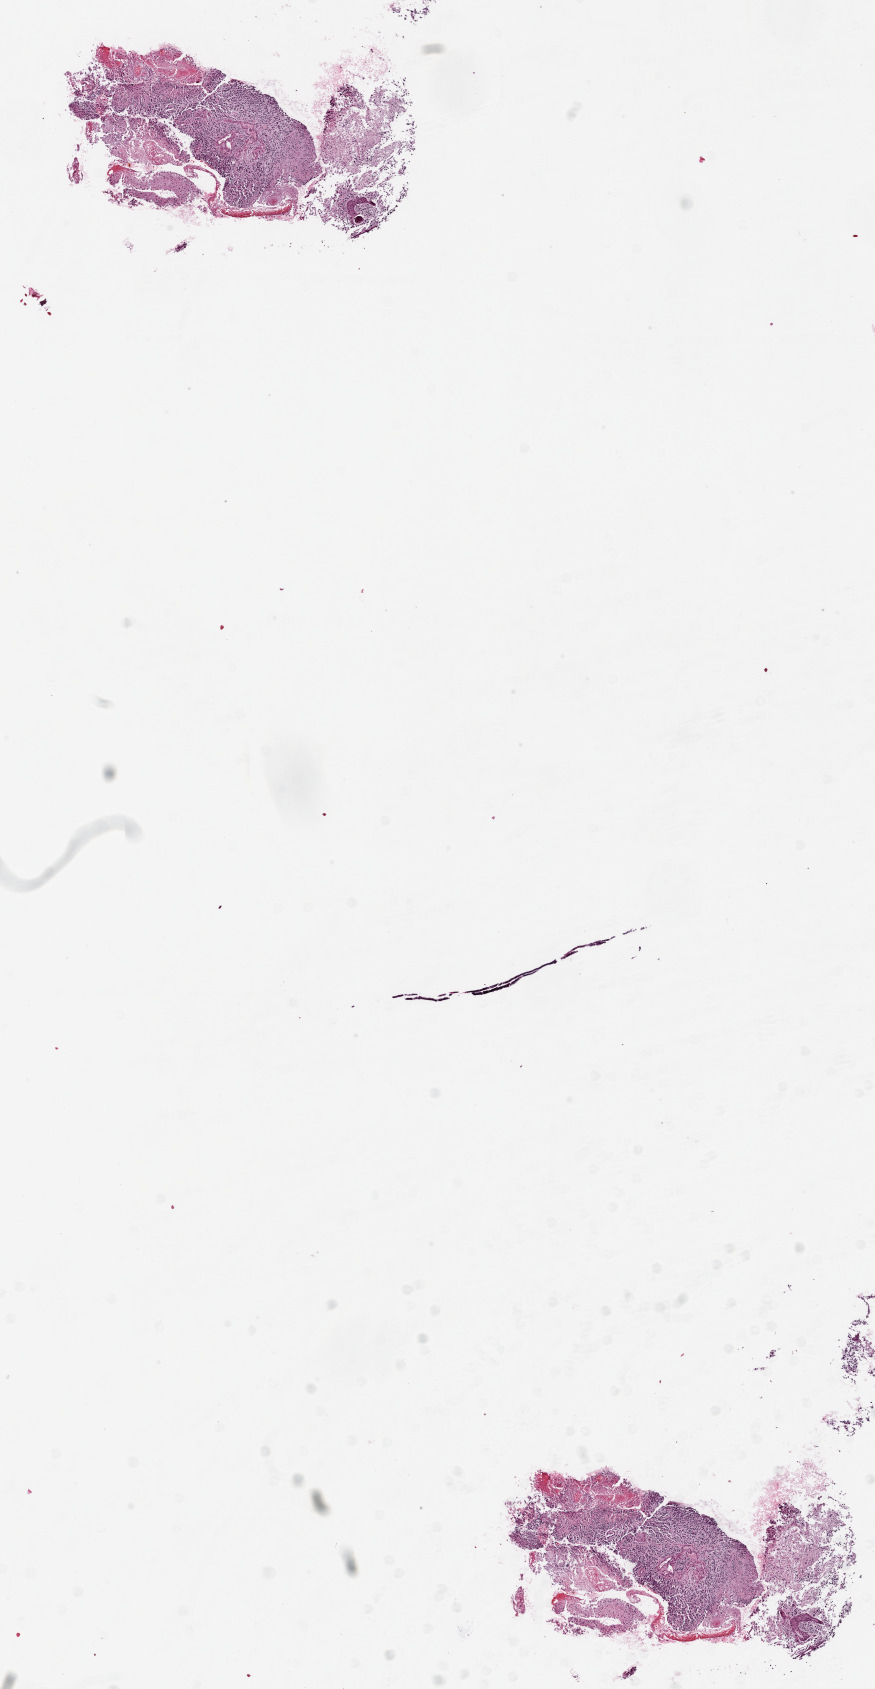
Digitized H&E-stained tissue section (whole slide), shown as a low-resolution overview of the whole scanned area (about 7.0 x 13.6 mm, slide scanned at 20x); formalin-fixed paraffin-embedded (FFPE) diagnostic section; sample: primary tumour, brain. Female patient; age at initial diagnosis 54 years.
Pathologic diagnosis: Glioblastoma.